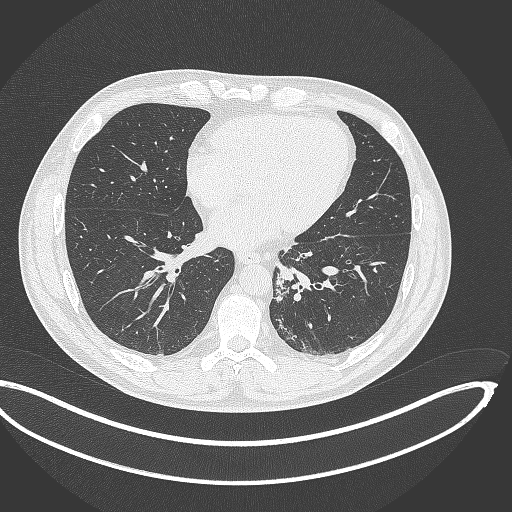
Chest CT, one axial slice; slice 133 of 362 in the series (ordered by position); reconstruction kernel B70f; 120 kVp; lung window (W 1500 / L -600 HU); 1 mm slice thickness; 512 × 512 image matrix, field of view 442 × 442 mm. Patient: male, 50 years. From the clinical record (not read from this slice): clinical TNM (as recorded): T2a N3 M0.
Outlined on this slice (bounding box drawn by a radiologist):
- lung tumour (recorded histology: squamous cell carcinoma): bounding box <273,272,294,304> (left, top, right, bottom; pixels)